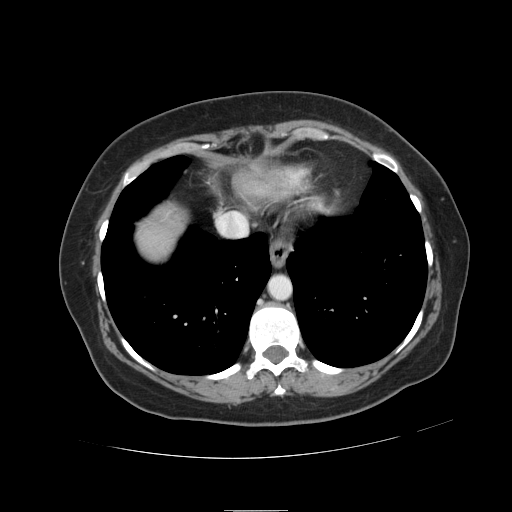
Contrast-enhanced abdominal CT, one axial slice. 120 kVp. Intravenous contrast given. Soft-tissue window (W 400 / L 40 HU). 2.5 mm slice thickness. 512 × 512 image matrix. Female patient, age 52 years. Case-level facts recorded for this patient, not image findings: diagnosis: colorectal cancer liver metastases, imaged before liver resection; multiple liver metastases: yes; largest metastasis: 6.3 cm; disease in both lobes: no.
Structures marked on this image (outlined manually by an expert reader):
- liver: bounding box (x1, y1, x2, y2) in pixels: (139, 209, 182, 259)